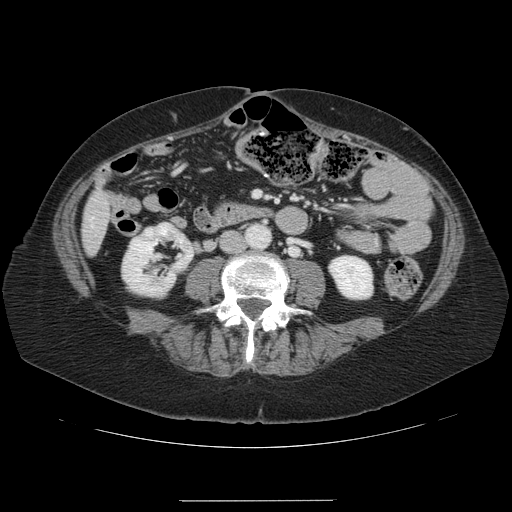
Contrast-enhanced abdominal CT, one axial slice; position 16 of 141 along the scan axis; 120 kVp; soft-tissue window (W 400 / L 40 HU); 512 × 512 image matrix, field of view 393 × 393 mm. Female patient, age 74 years. From the clinical record (not read from this slice): diagnosis: colorectal cancer liver metastases, imaged before liver resection; multiple liver metastases: yes; largest metastasis: 7 cm; chemotherapy before resection: no.
Structures marked on this image (expert manual segmentation):
- liver: box from (x=83, y=191) to (x=111, y=253) px
- planned liver remnant (the part of the liver to remain after resection): (x=88, y=191)–(x=111, y=244)